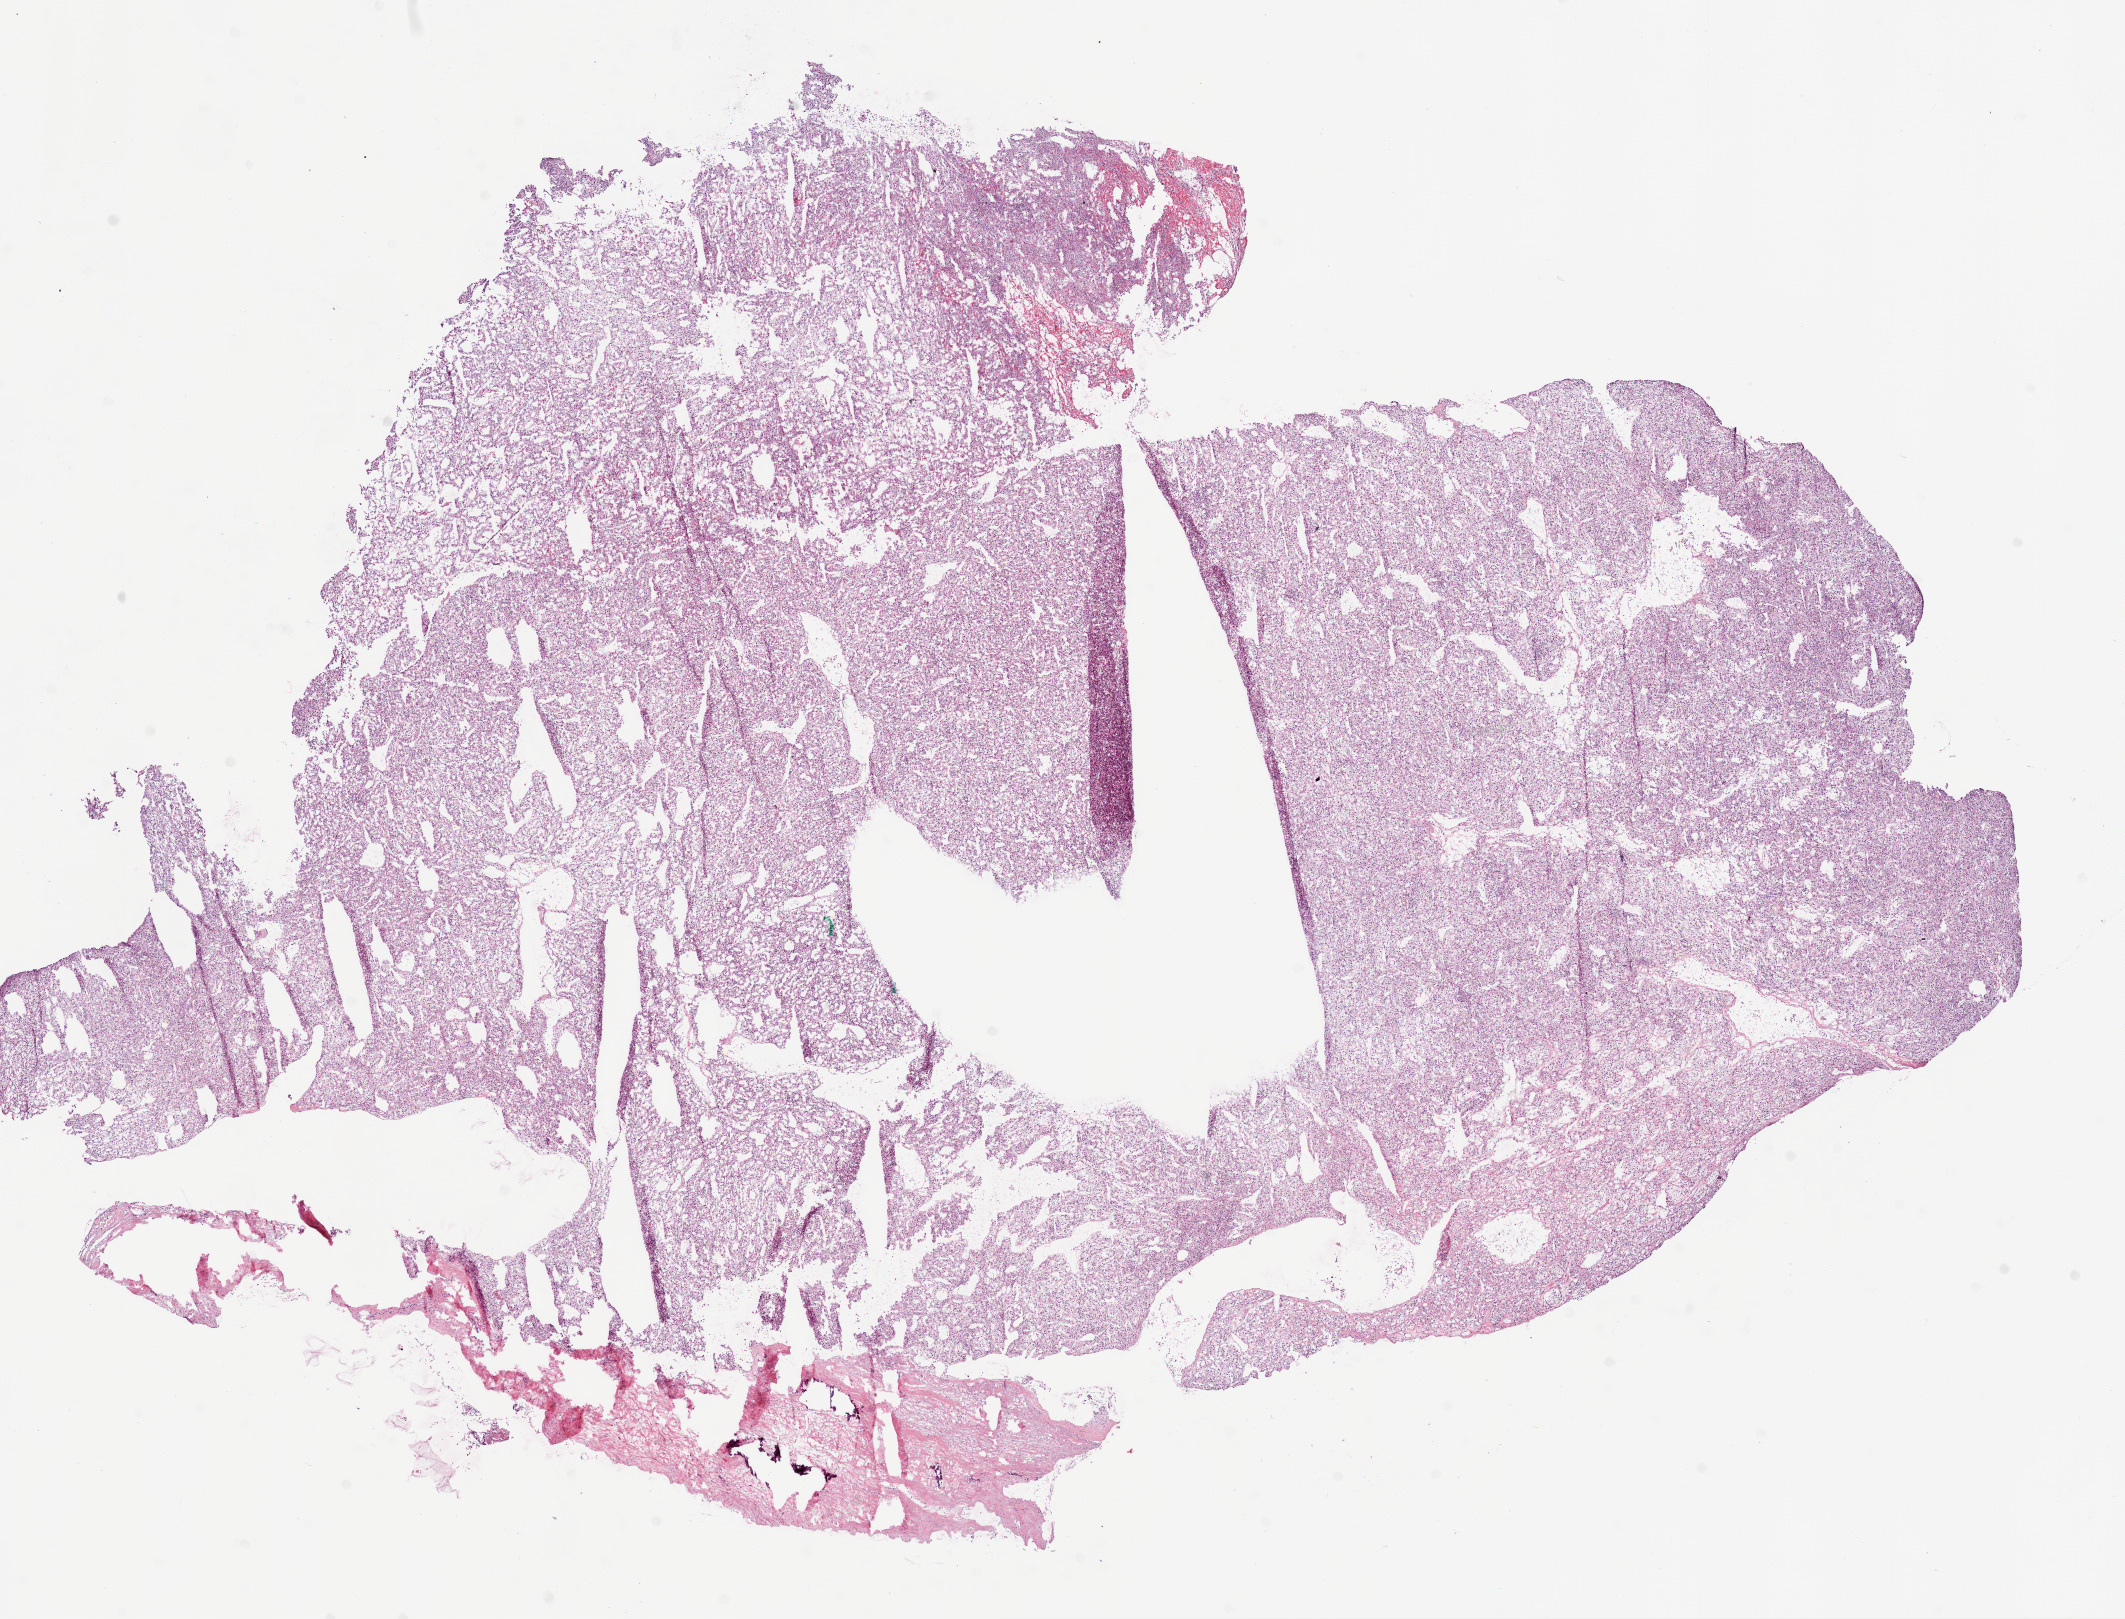
H&E-stained whole-slide image — whole scanned area (about 17.1 x 13.0 mm, acquisition: 20x scan) shown as a low-resolution overview; frozen section from the bottom of the tissue portion; primary tumour sample from the kidney. Male, age 66 years at initial diagnosis. Histologic grade: G4 (undifferentiated). Slide review estimates, as recorded: tumour cells 90%, tumour nuclei 85%, normal cells 0%, stromal cells 10%, necrosis 0%.
- histologic diagnosis: Clear cell adenocarcinoma, NOS
- laterality: left
- AJCC pathologic stage: I